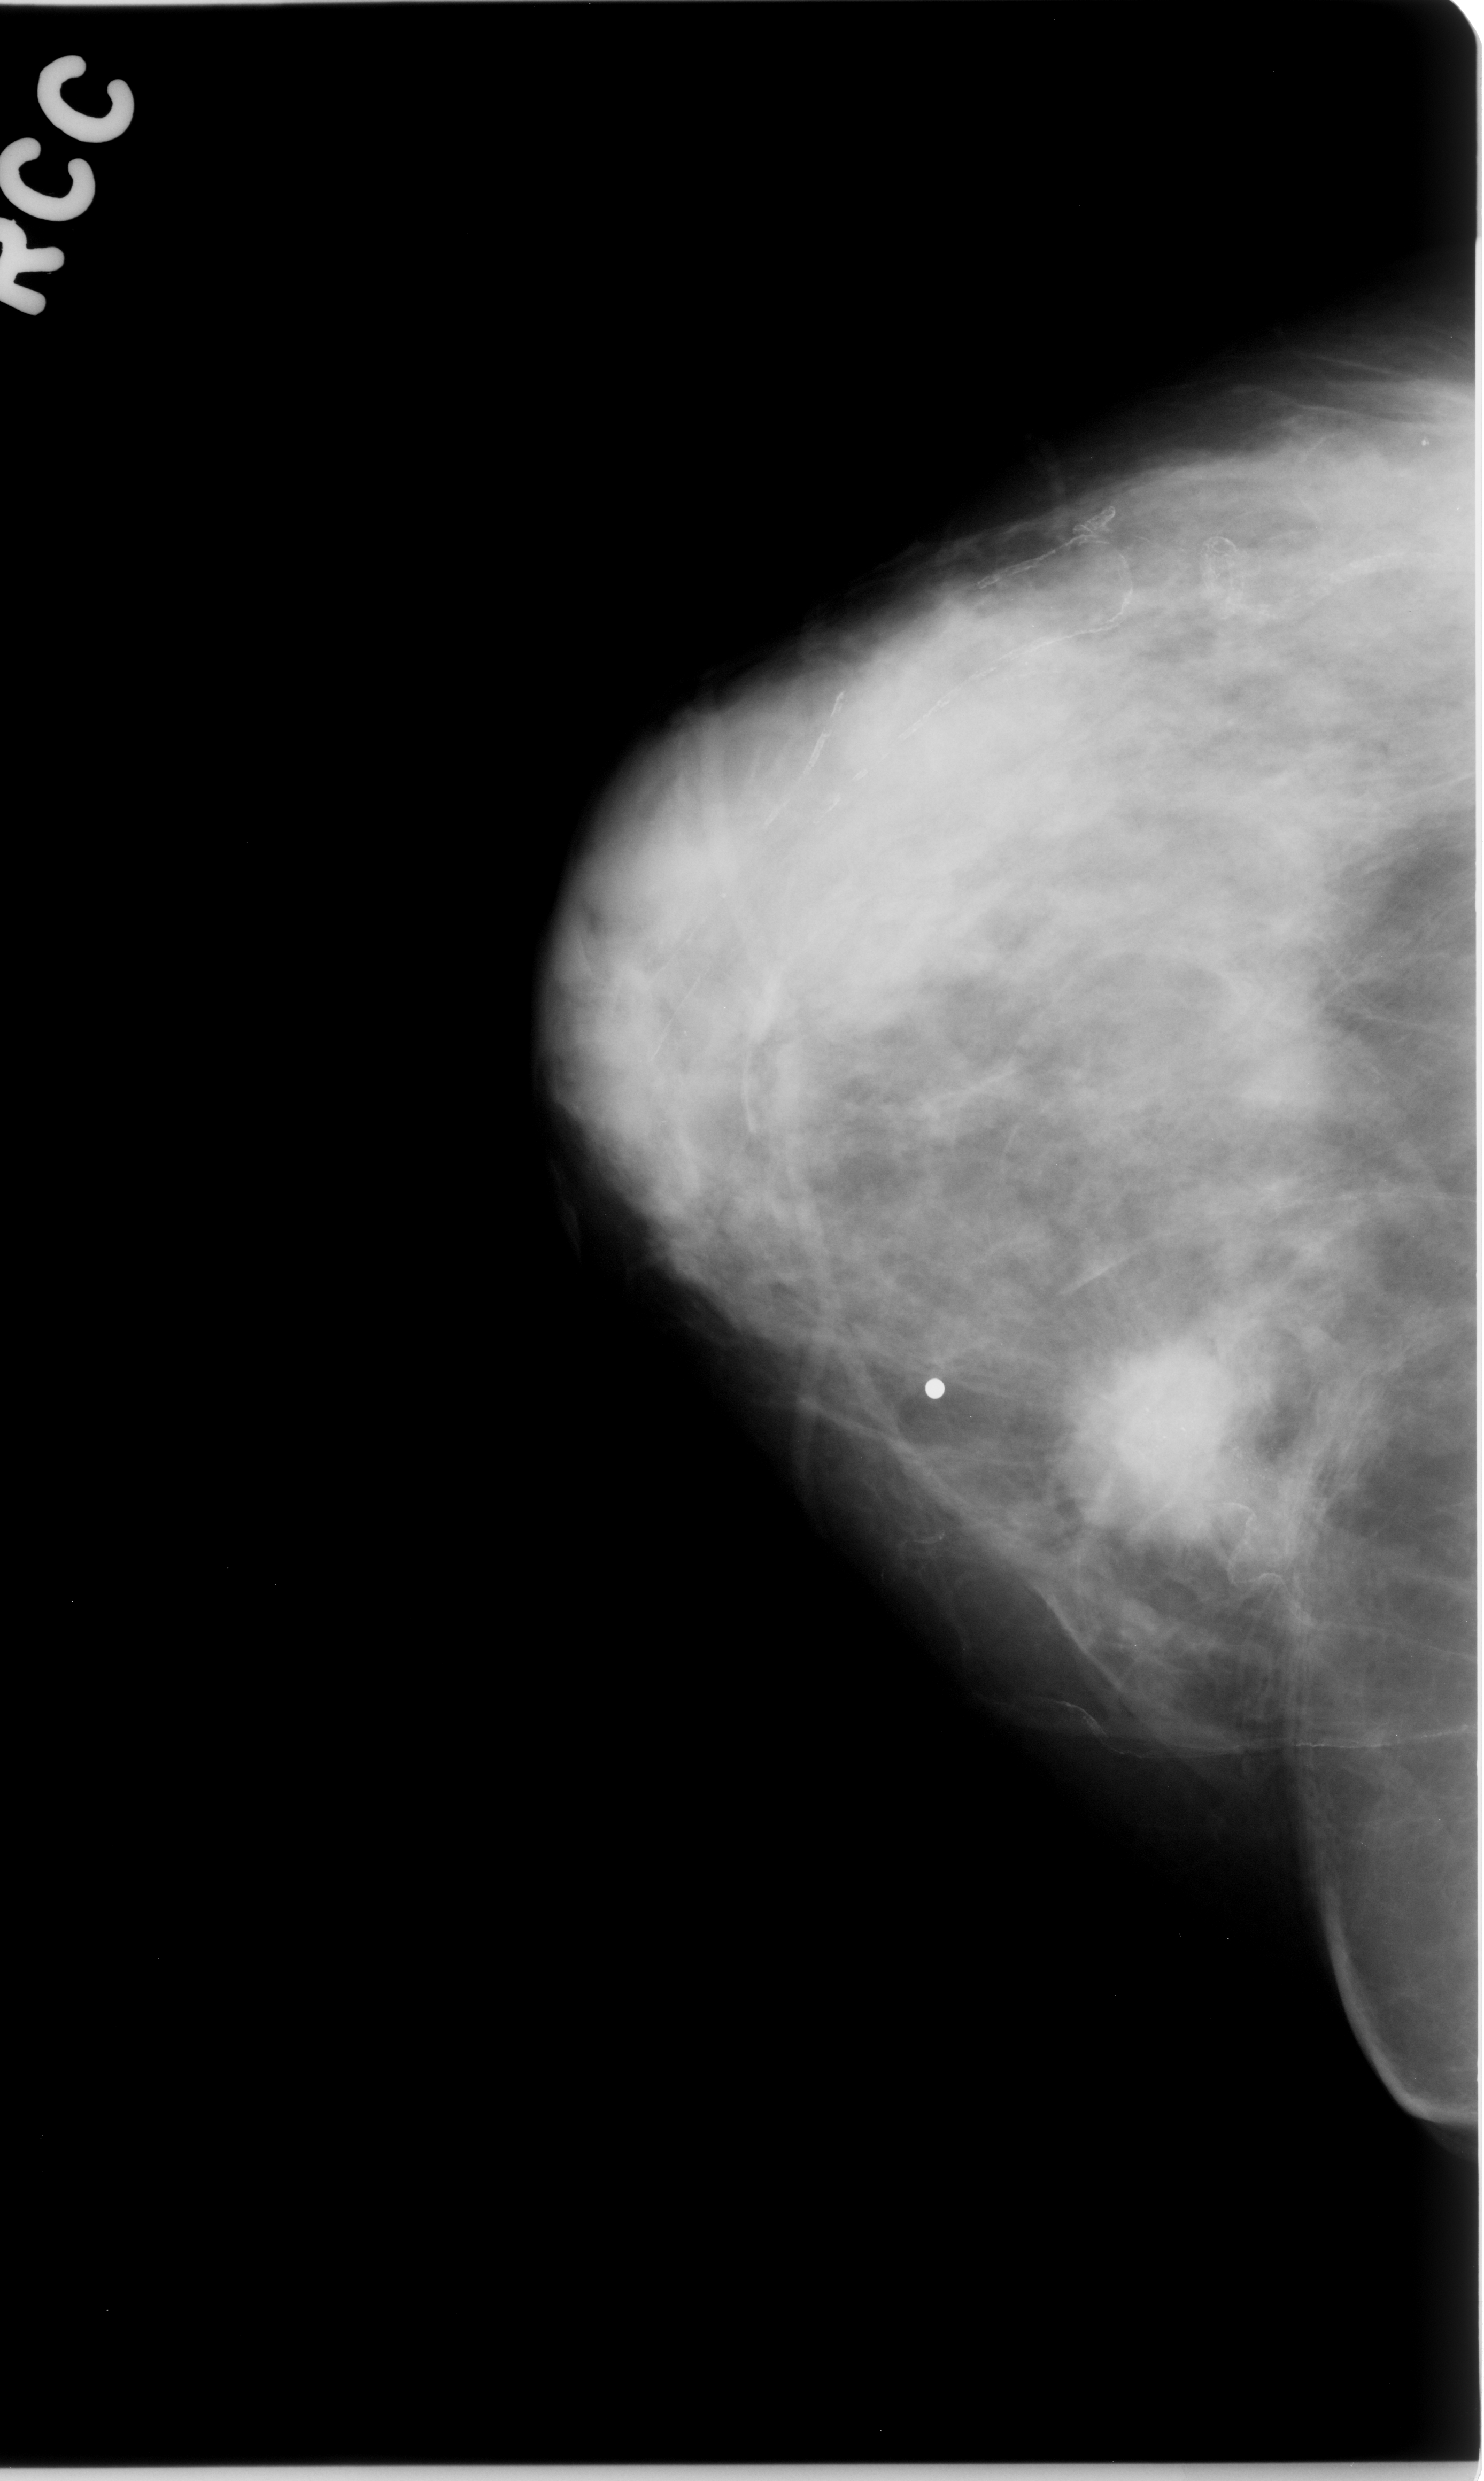
Scanned film-screen mammogram; right breast; CC view; breast composition: heterogeneously dense (BI-RADS density category 3 of 4).
Radiologist-marked abnormalities on this image: calcifications, morphology amorphous, distribution clustered; BI-RADS assessment category 5; pathology result (as recorded, not read from the image): malignant.